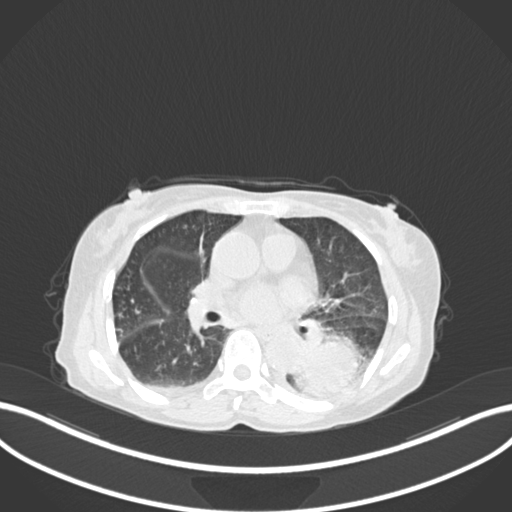
Chest CT, one axial slice; position 84 of 233 along the scan axis; lung window (W 1500 / L -600 HU); 1 mm slice thickness; 512 × 512 image matrix, field of view 400 × 400 mm. Female patient, age 78 years. Case-level facts recorded for this patient, not image findings: clinical TNM (as recorded): T3 N0 M1.
Structures marked on this image (rectangle marked by the reading radiologist):
- lung tumour (recorded histology: squamous cell carcinoma): bounding box (x1, y1, x2, y2) in pixels: (295, 333, 365, 401)